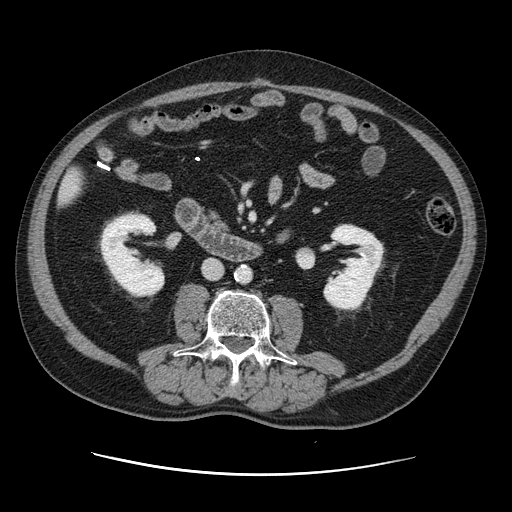
Contrast-enhanced abdominal CT, one axial slice; position 29 of 141 along the scan axis; 120 kVp; intravenous contrast given; soft-tissue window (W 400 / L 40 HU); 2.5 mm slice thickness; 512 × 512 image matrix, field of view 395 × 395 mm. Male patient, age 72 years. Case-level facts recorded for this patient, not image findings: diagnosis: colorectal cancer liver metastases, imaged before liver resection; multiple liver metastases: yes; largest metastasis: 5.4 cm; disease in both lobes: yes.
Outlined on this slice (expert manual segmentation):
- liver: bounding box [x1, y1, x2, y2] px = [61, 171, 83, 202]
- planned liver remnant (the part of the liver to remain after resection): [61, 171, 83, 203]